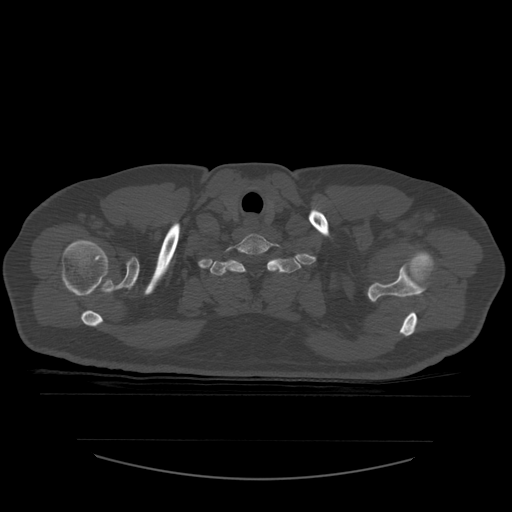
CT including the spine, one axial slice. Slice 475 of 532 in the series (ordered by position). Reconstruction kernel STANDARD. 120 kVp. Bone window (W 1800 / L 400 HU). 1.25 mm slice thickness. 512 × 512 image matrix, field of view 441 × 441 mm. Patient age 44 years. Case-level facts recorded for this patient, not image findings: primary cancer: soft tissue sarcoma.
Structures marked on this image (semi-automatic segmentation, software-assisted and operator-edited):
- T1 vertebra: bounding box (x1, y1, x2, y2) in pixels: (210, 258, 301, 276)